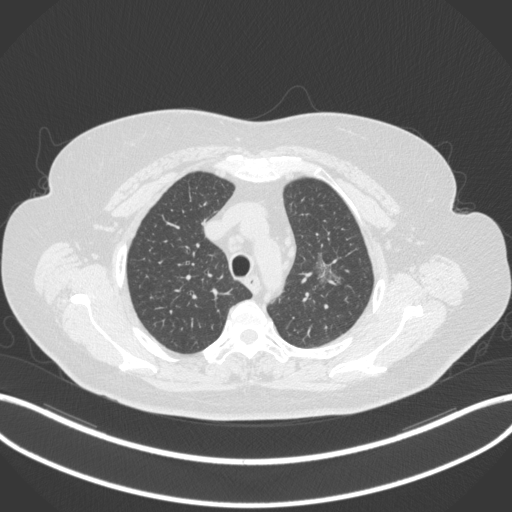
Chest CT, one axial slice; position 263 of 310 along the scan axis; reconstruction kernel B31f; 120 kVp; lung window (W 1500 / L -600 HU); 1 mm slice thickness; 512 × 512 image matrix, field of view 400 × 400 mm. Patient: female, 70 years. Case-level facts recorded for this patient, not image findings: clinical TNM (as recorded): T1c N0 M0.
Annotated regions visible in this slice (rectangle marked by the reading radiologist):
- lung tumour (recorded histology: adenocarcinoma): box from (x=312, y=251) to (x=343, y=292) px